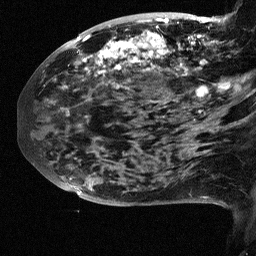
Breast MRI (dynamic contrast-enhanced), one sagittal slice; position 25 of 64 along the scan axis; dynamic contrast-enhanced study with each time point stored as its own series, time point 2 of 3 at this slice position (early post-contrast, ordered by acquisition time); 1.5 T; TE 4.5 ms, TR 11 ms; 2.5 mm slice thickness; 256 × 256 image matrix, field of view 200 × 200 mm. Patient: female, 38 years. From the clinical record (not read from this slice): setting: breast cancer imaged before/during neoadjuvant chemotherapy; receptor status: HR-positive, HER2-negative.
Outlined on this slice (semi-automatically segmented with operator editing):
- analysis volume of interest (the breast-tissue region the enhancement analysis was run in; not a lesion): bounding box (x1, y1, x2, y2) in pixels: (88, 18, 252, 126)
- tumour enhancement mask (voxels above the 90 % enhancement threshold inside the analysis volume of interest): (88, 18, 249, 112)